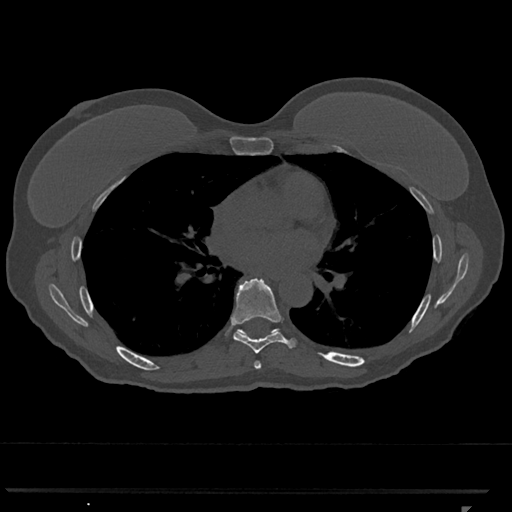
CT including the spine, one axial slice; position 706 of 793 along the scan axis; 120 kVp; bone window (W 1800 / L 400 HU); 0.5 mm slice thickness; 512 × 512 image matrix, field of view 380 × 380 mm. Patient: female, 62 years. From the clinical record (not read from this slice): primary cancer: renal.
Outlined on this slice (semi-automatic segmentation, software-assisted and operator-edited):
- T6 vertebra: bounding box <254,361,262,369> (left, top, right, bottom; pixels)
- T7 vertebra: <231,278,298,354>
- T8 vertebra: <241,330,271,333>